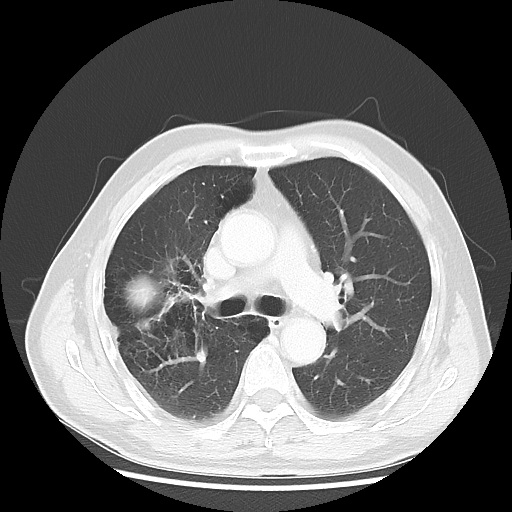
Chest CT, one axial slice; reconstruction kernel LUNG; 120 kVp; lung window (W 1500 / L -600 HU); 5 mm slice thickness; 512 × 512 image matrix. Patient: male, 69 years. From the clinical record (not read from this slice): clinical TNM (as recorded): T3 N0 M0; histopathological grade: G3.
Outlined on this slice (bounding box drawn by a radiologist):
- lung tumour (recorded histology: adenocarcinoma): bounding box [x1, y1, x2, y2] px = [115, 268, 168, 321]